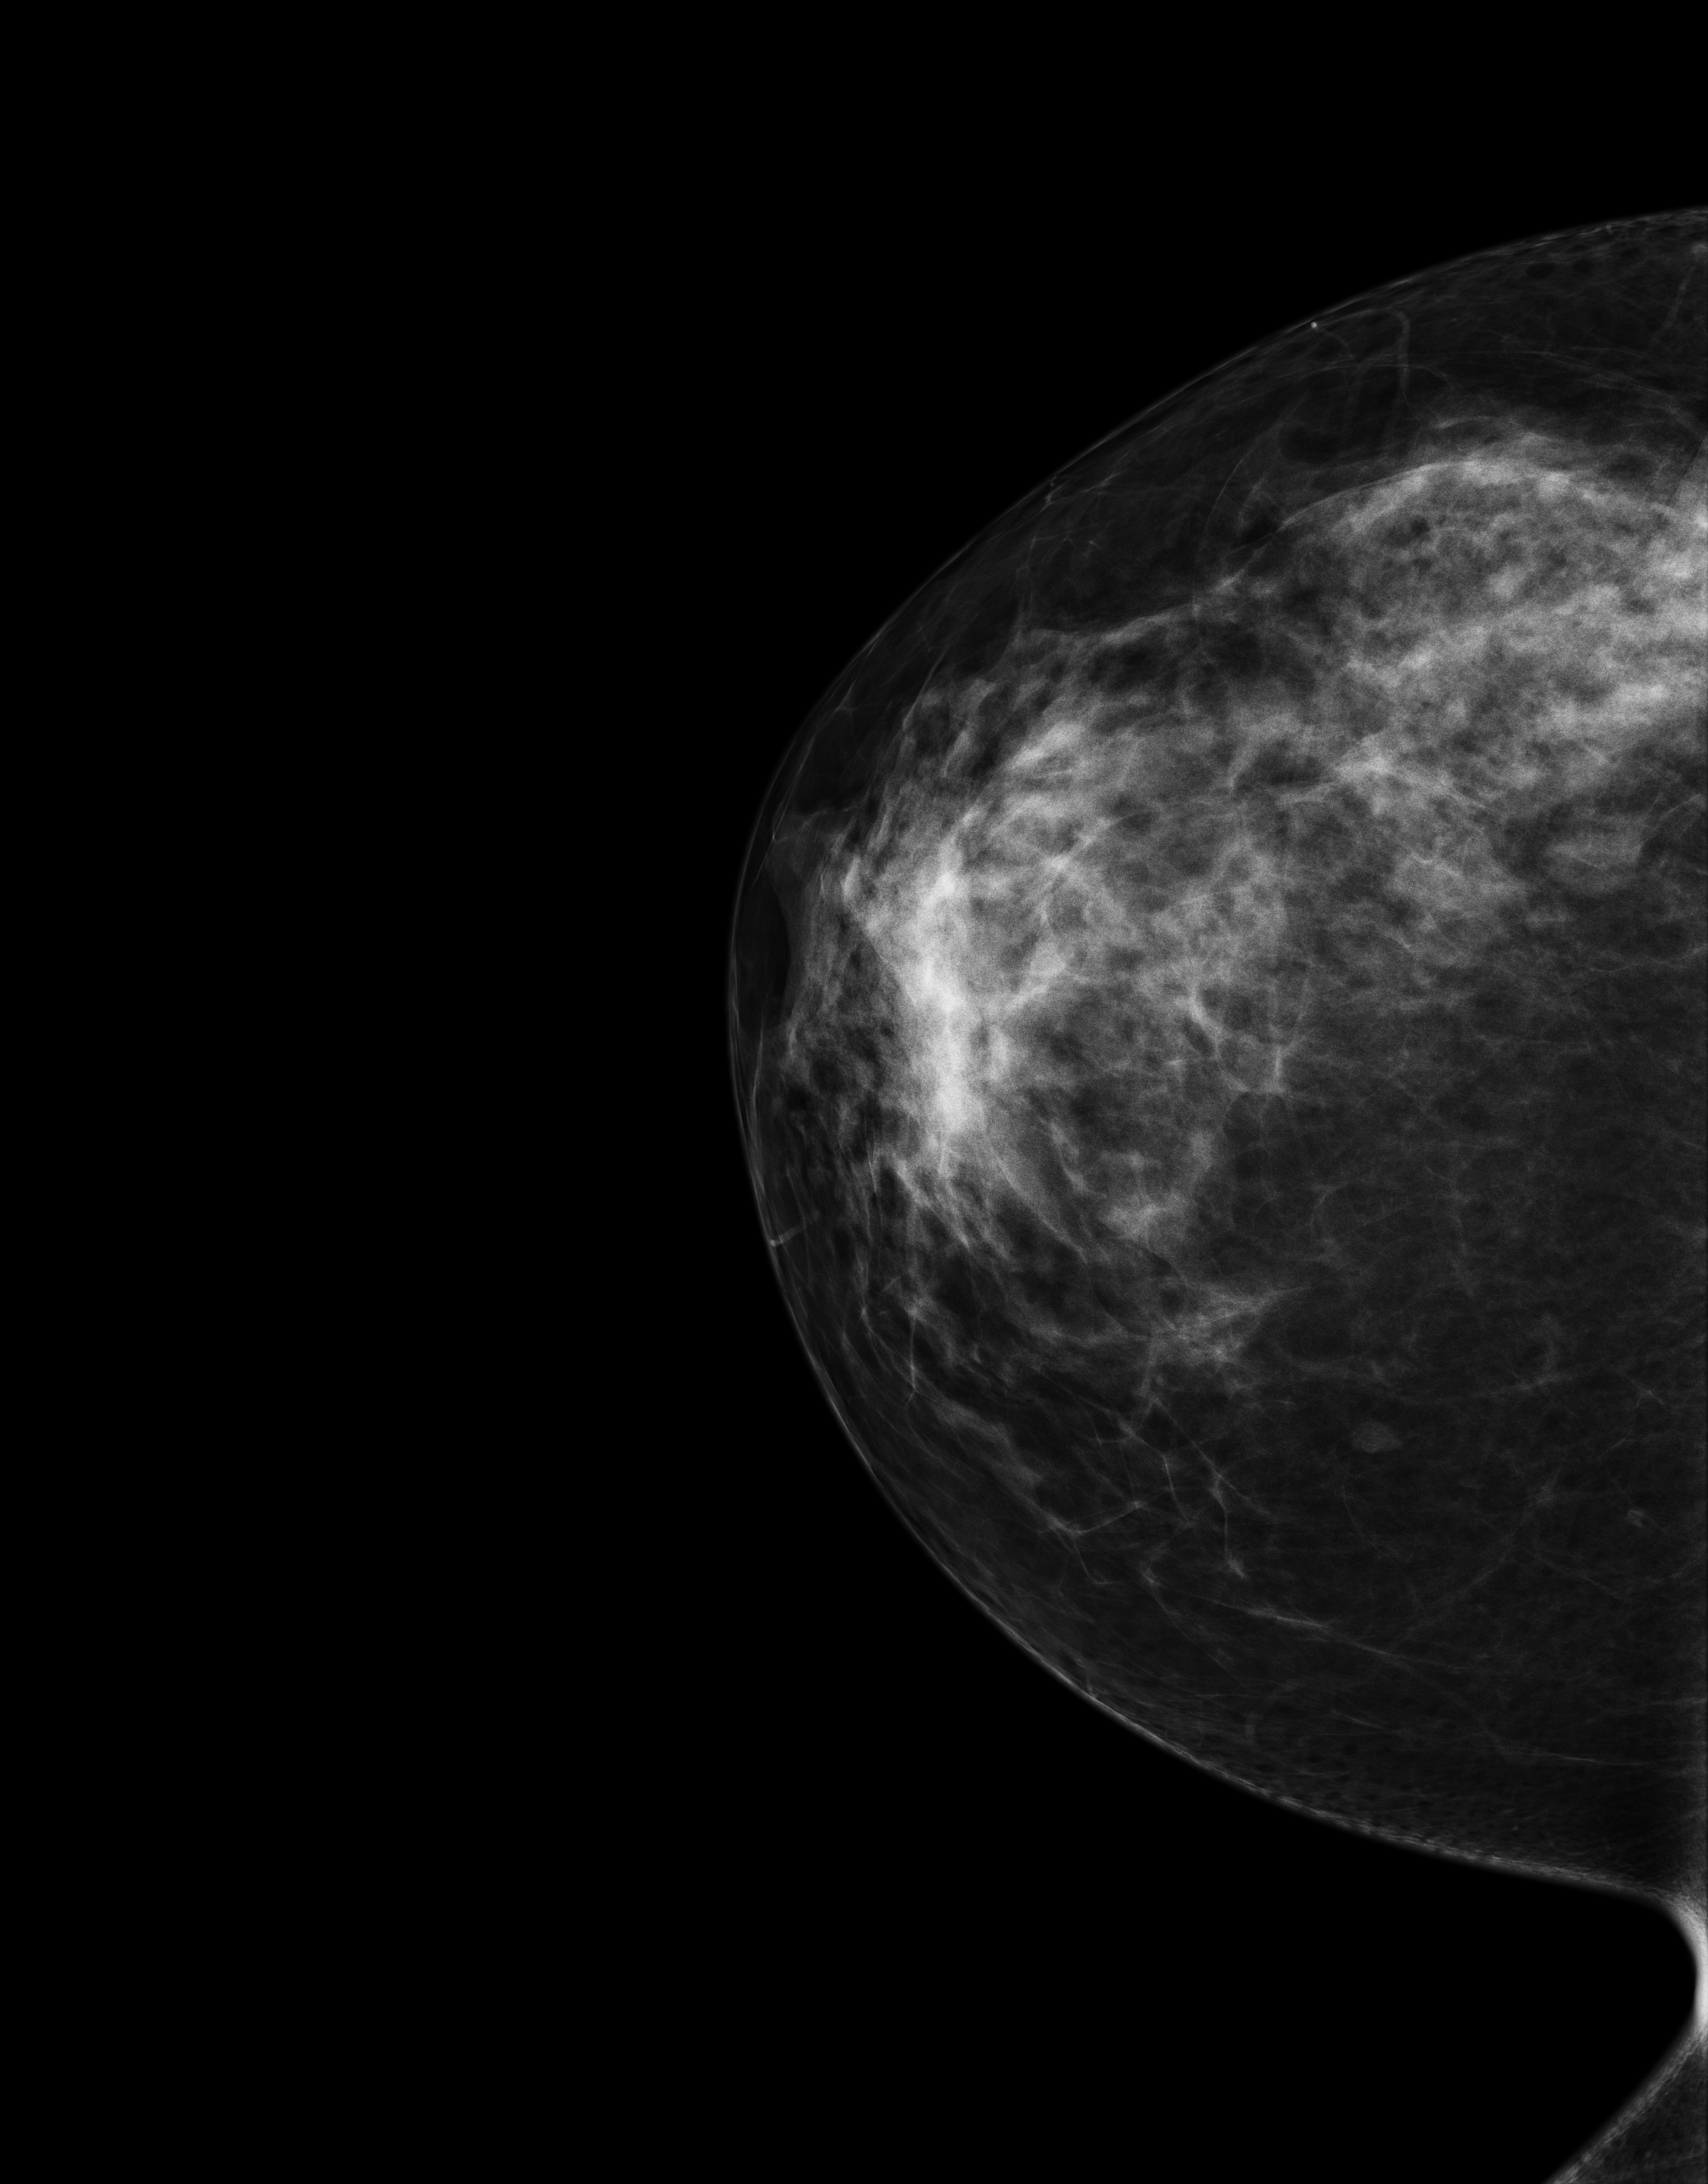
Full-field digital mammogram (FFDM); right breast; cranio-caudal projection; annual screening mammography examination; compressed breast thickness 81 mm; system: Senographe Essential ADS_56.21.3. Patient: female, 42 years.
Final BI-RADS assessment for this screening round (tomosynthesis exam, both breasts): category 1.